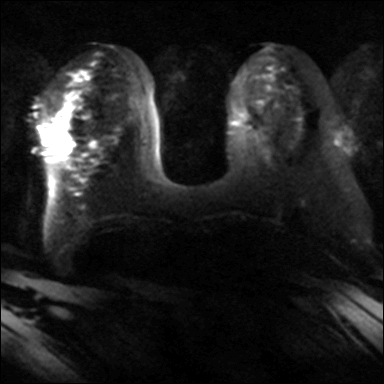
Breast MRI, one axial slice. Slice 15 of 40 in the series (ordered by position). Diffusion-weighted series; image 2 of 4 stored at this slice position (different b-values; order by instance number). 3 T. 4 mm slice thickness. 384 × 384 image matrix. Female patient.
Outlined on this slice (manually delineated by an expert):
- tumour on diffusion-weighted imaging: box from (x=47, y=125) to (x=69, y=148) px